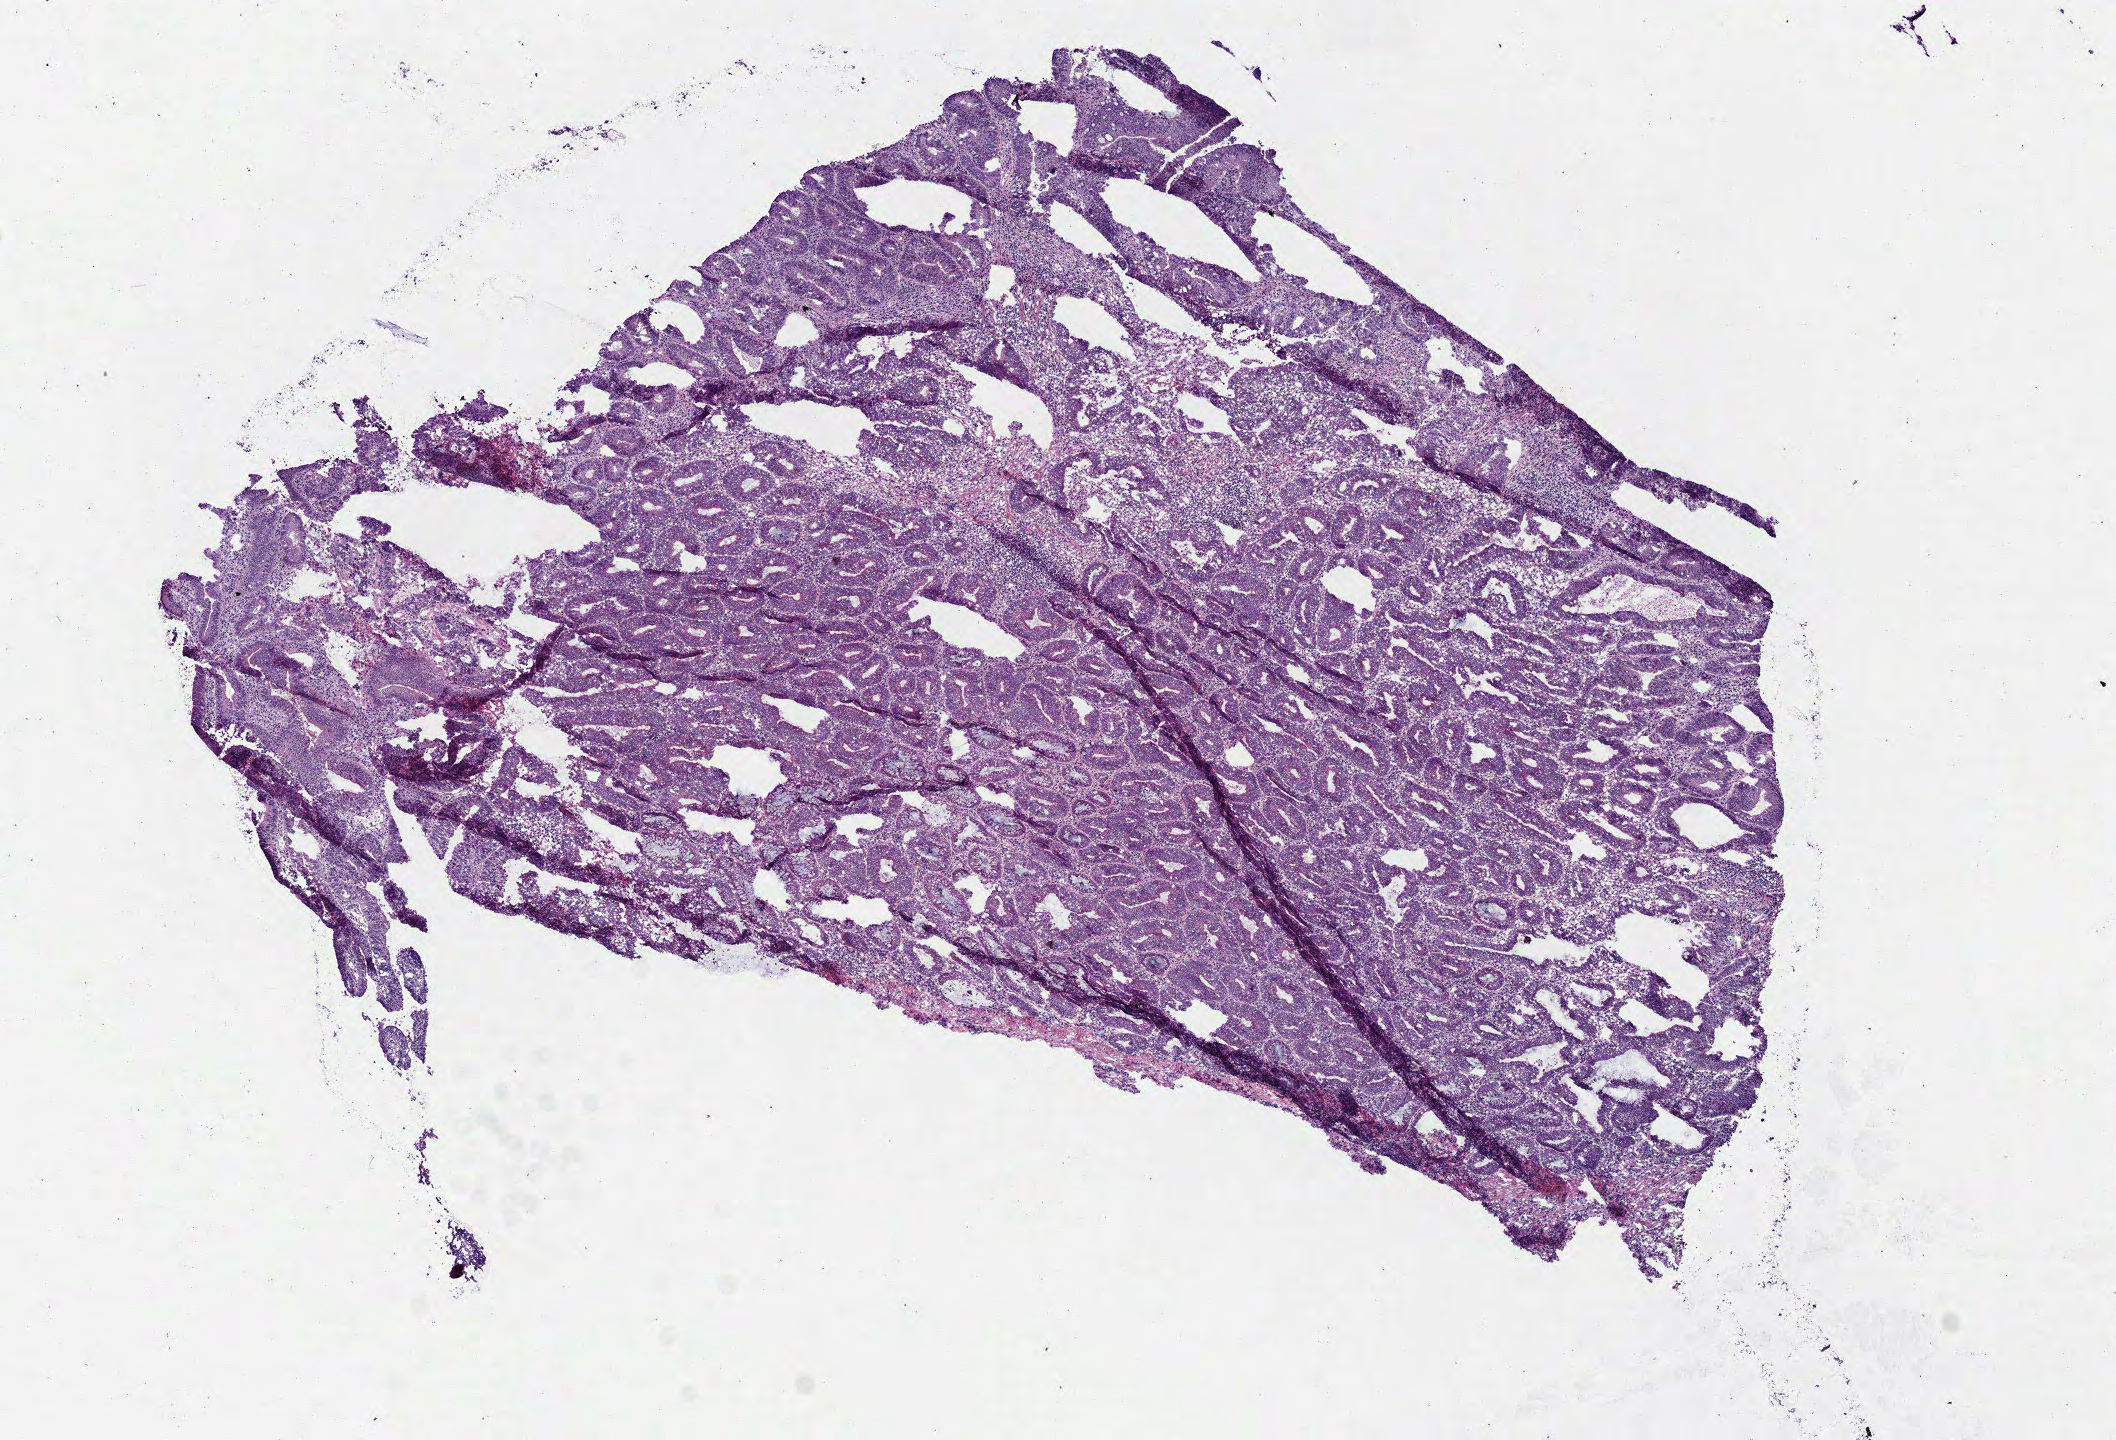
Digitized H&E-stained tissue section (whole slide), low-resolution overview of the scanned area, about 8.3 x 5.7 mm (acquisition: 40x scan), frozen section, sample: primary tumour, rectum. Patient: female, age at initial diagnosis 77 years. Composition of this section per pathologist review: tumour cells 80%, tumour nuclei 75%, normal cells 10%, stromal cells 10%, necrosis 0%.
• pathologic diagnosis: Adenocarcinoma in tubulovillous adenoma